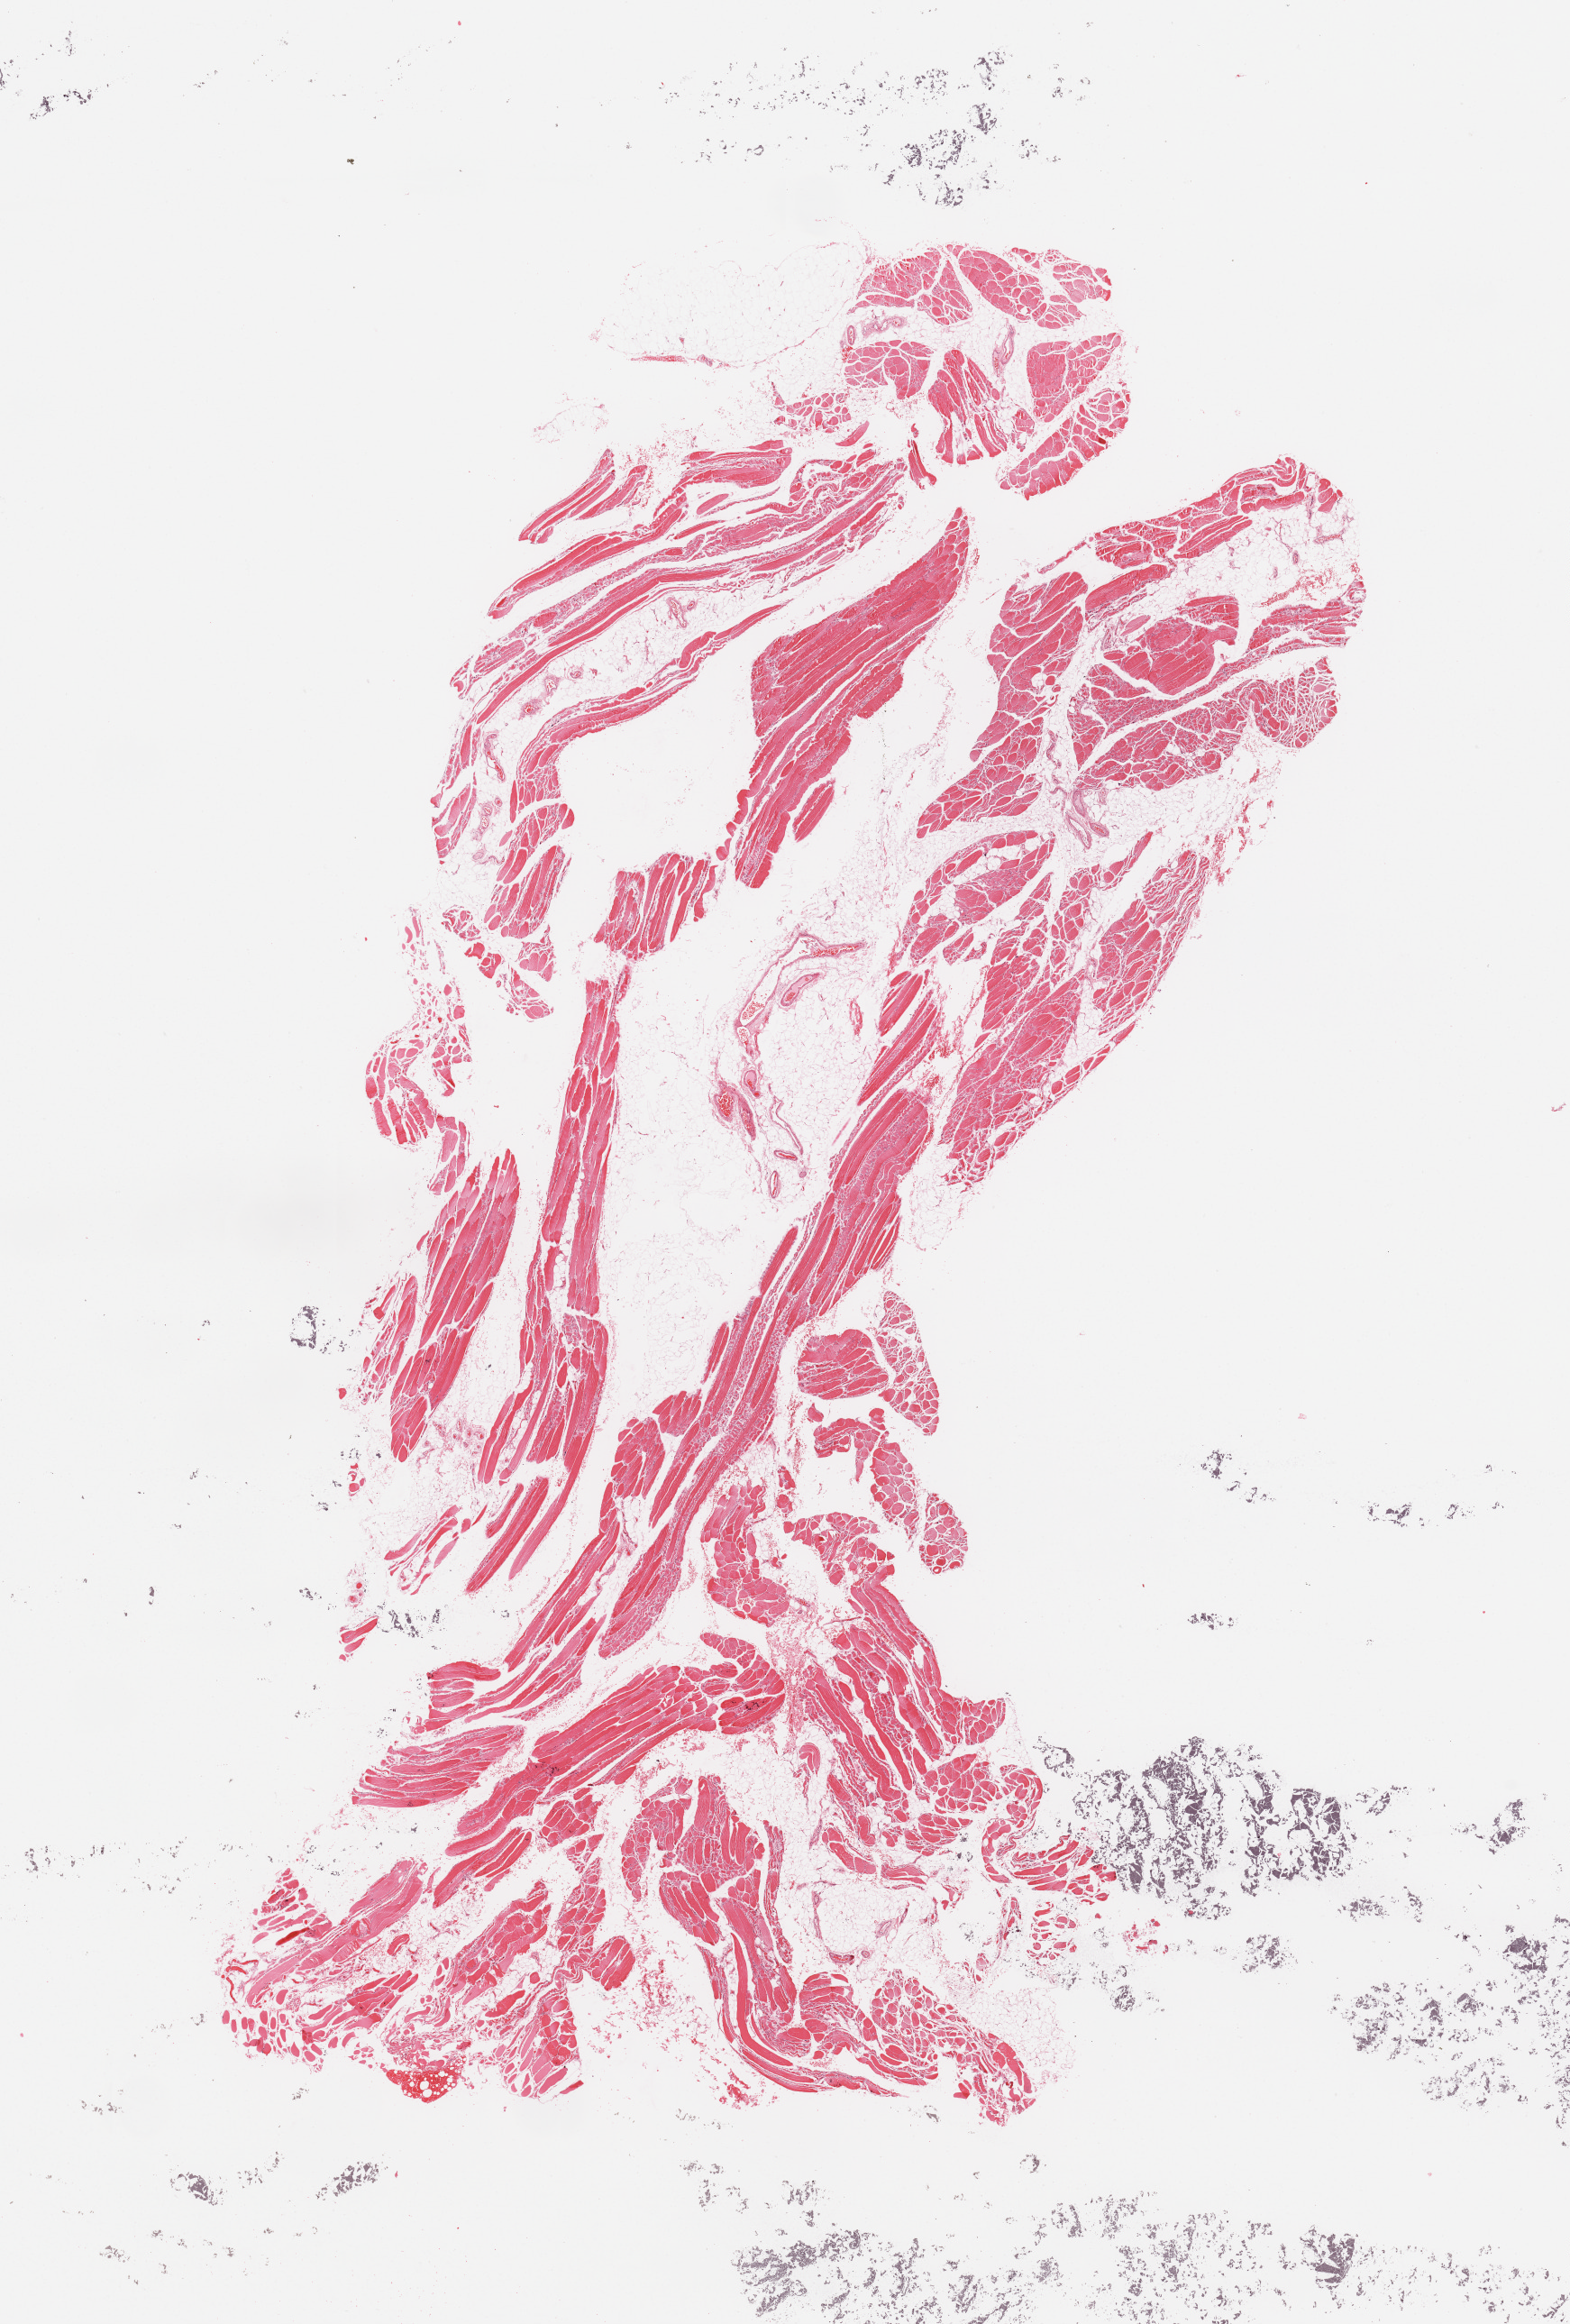
Whole-slide histology image, H&E-stained — low-resolution overview of the scanned area, about 13.8 x 20.4 mm; normal (non-tumour) tissue sample. Male, 67 y/o.
* this section: normal (non-tumour) tissue from the same patient
* patient diagnosis (cohort enrolment): sarcoma (site not recorded at cohort level)